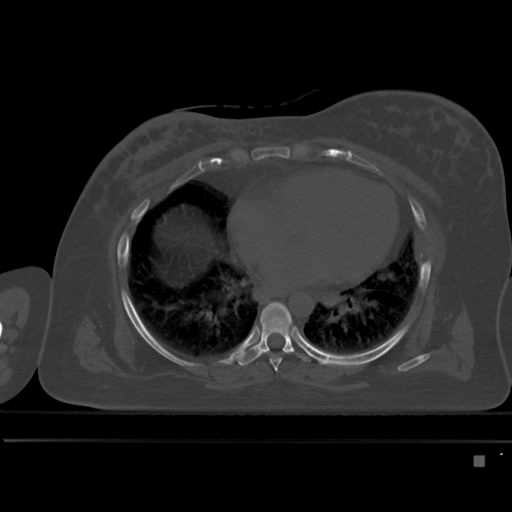
CT including the spine, one axial slice. Slice 297 of 495 in the series (ordered by position). Bone window (W 1800 / L 400 HU). 512 × 512 image matrix, field of view 404 × 404 mm. Female patient, age 33 years. Case-level facts recorded for this patient, not image findings: primary cancer: breast; vertebrae with lytic lesions (as recorded): T1.
Outlined on this slice (semi-automatic segmentation, software-assisted and operator-edited):
- T6 vertebra: bounding box <270,349,296,372> (left, top, right, bottom; pixels)
- T7 vertebra: <240,302,313,366>